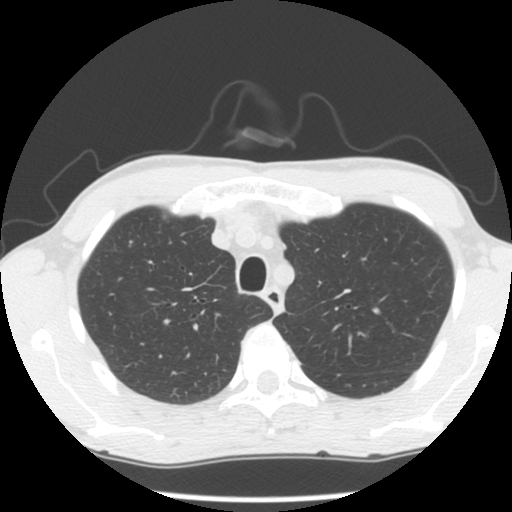
Axial slice from a low-dose chest CT screening exam, second annual screen, lung window (W 1500 / L -600 HU), 512 × 512 image matrix, field of view 318 × 318 mm. Male participant, aged 56 years at enrolment.
- Lesion marked by an expert reader, bounding box <105,223,149,267> (left, top, right, bottom; pixels).
- Screening reader's record for this exam: no non-calcified nodule ≥4 mm recorded.
- Lung cancer was diagnosed 345 days after this screen: small cell carcinoma, NOS, right upper lobe, stage IV (AJCC 6th edition).